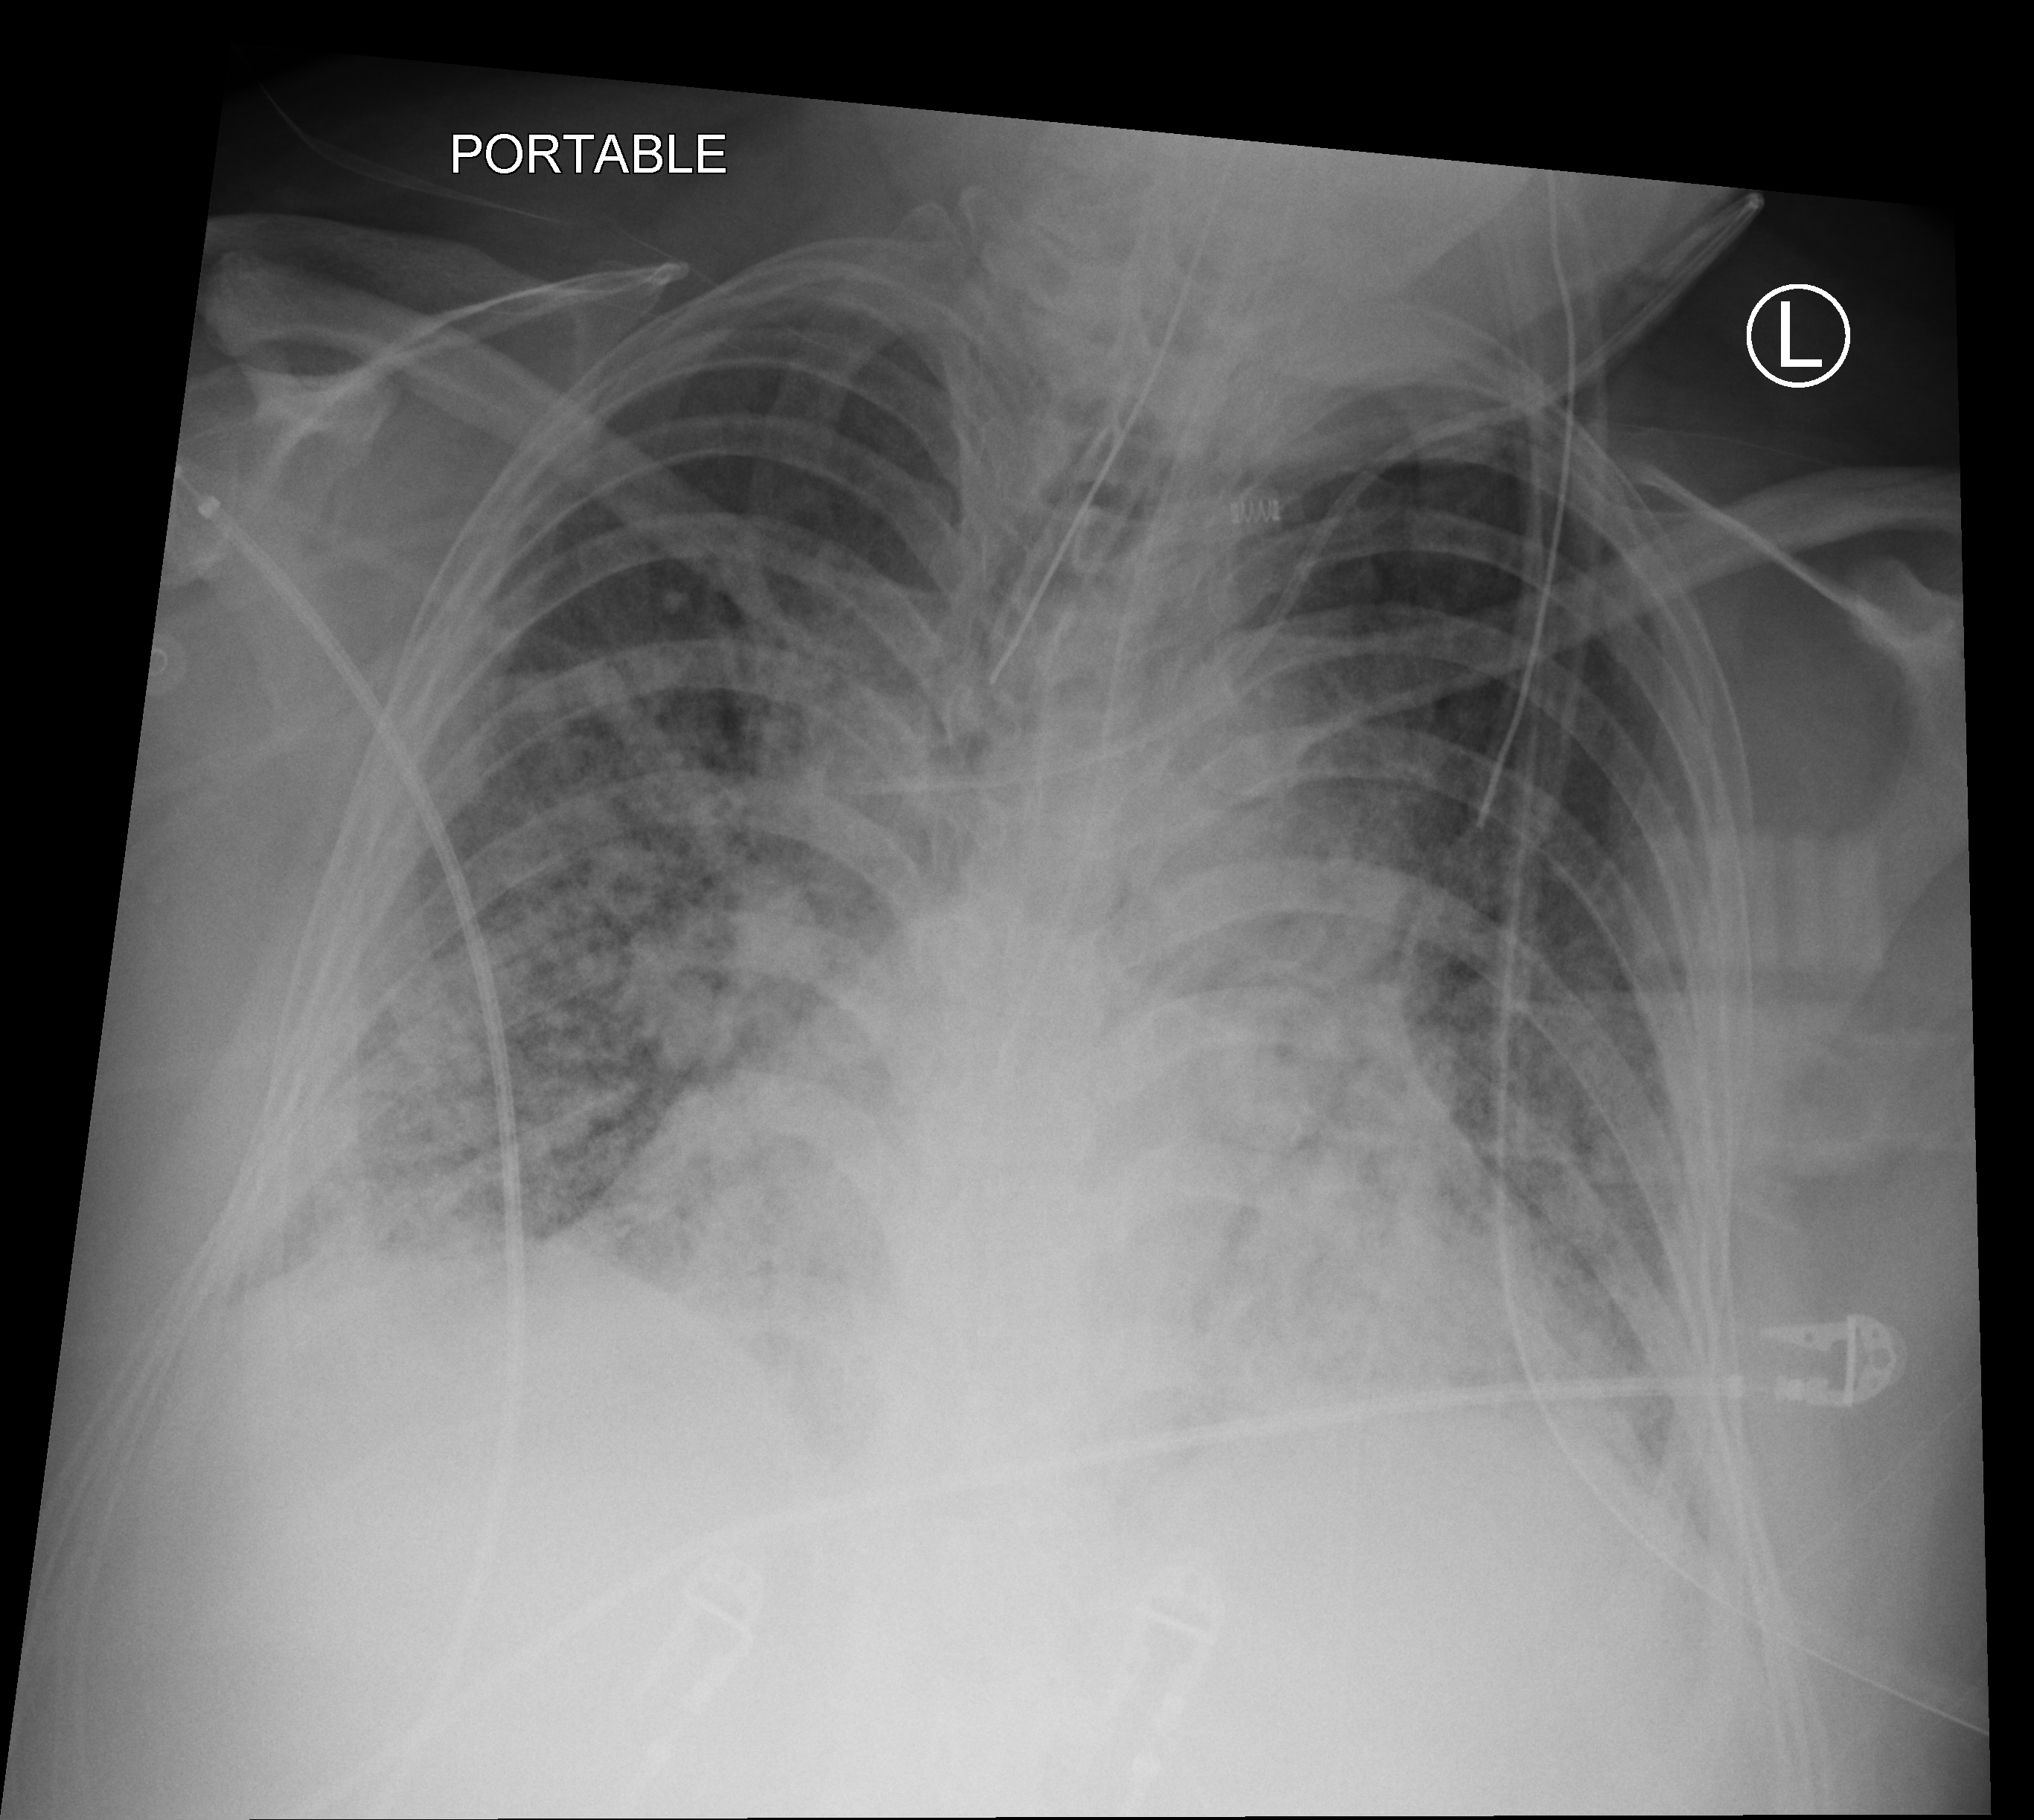
Bedside chest radiograph (computed radiography), anteroposterior (AP) projection. Patient hospitalised with COVID-19, aged 18–59 years.
From the hospital-stay record, not from the radiograph (when in the stay this image was taken is not recorded):
- hypertension (admission record): no